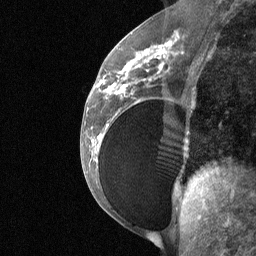
Breast MRI (dynamic contrast-enhanced), one sagittal slice; position 32 of 64 along the scan axis; dynamic contrast-enhanced study with each time point stored as its own series, time point 2 of 3 at this slice position (early post-contrast, ordered by acquisition time); 1.5 T; TE 4.8 ms, TR 27 ms; 2 mm slice thickness; 256 × 256 image matrix, field of view 200 × 200 mm. Female patient, age 34 years. Case-level facts recorded for this patient, not image findings: setting: breast cancer imaged before/during neoadjuvant chemotherapy; receptor status: HR-positive, HER2-negative.
Outlined on this slice (semi-automatic segmentation, software-assisted and operator-edited):
- analysis volume of interest (the breast-tissue region the enhancement analysis was run in; not a lesion): bounding box <92,50,188,185> (left, top, right, bottom; pixels)
- tumour enhancement mask (voxels above the 90 % enhancement threshold inside the analysis volume of interest): <92,50,164,141>